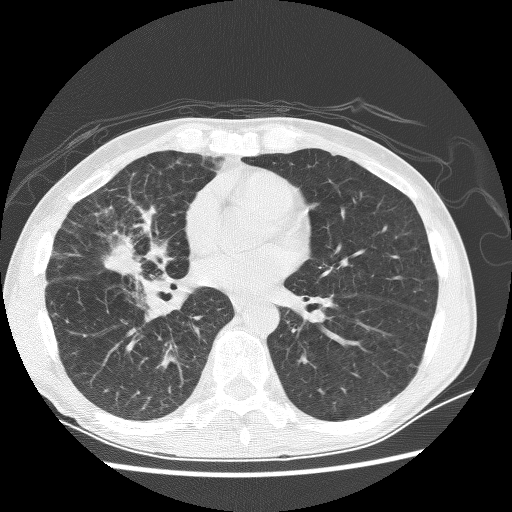
Low-dose screening chest CT, axial slice. First (baseline) screen. Lung window (W 1500 / L -600 HU). 512 × 512 image matrix, field of view 340 × 340 mm. Male, age 67 years at enrolment. Current smoker at enrolment.
Lesion marked by an expert reader, bounding box [x1, y1, x2, y2] px = [81, 219, 175, 290]. Reader record for this screening exam (exam-level; its link to the box is not recorded): non-calcified nodule or mass ≥4 mm, right middle lobe, 28 × 18 mm, spiculated (stellate) margins, soft tissue attenuation. Official screen result: positive, change unspecified: nodule(s) >= 4 mm or enlarging nodule(s), mass(es), or other non-specific abnormalities suspicious for lung cancer. Later outcome: lung cancer diagnosed 69 days after this screen — adenocarcinoma, NOS, right middle lobe, stage IV (AJCC 6th edition), 60 mm at pathology.